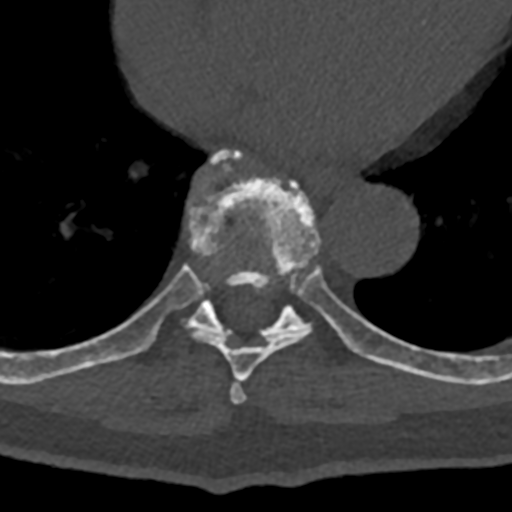
CT including the spine, one axial slice. Position 686 of 797 along the scan axis. Reconstruction kernel Br40s/3. 120 kVp. Bone window (W 1800 / L 400 HU). 0.5 mm slice thickness. 512 × 512 image matrix, field of view 160 × 160 mm. Patient: male, 74 years. From the clinical record (not read from this slice): primary cancer: renal; vertebrae with lytic lesions (as recorded): T10, L1, L2, L3, L4, L5.
Annotated regions visible in this slice (semi-automatically segmented with operator editing):
- T7 vertebra: bounding box [x1, y1, x2, y2] px = [230, 380, 247, 404]
- T8 vertebra: [70, 153, 365, 381]
- T9 vertebra: [108, 149, 432, 379]